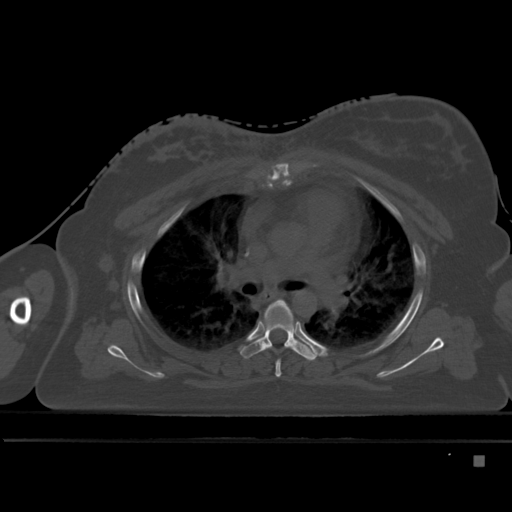
CT including the spine, one axial slice; position 324 of 495 along the scan axis; bone window (W 1800 / L 400 HU); 512 × 512 image matrix. Female patient, age 33 years. Case-level facts recorded for this patient, not image findings: primary cancer: breast; vertebrae with lytic lesions (as recorded): T1.
Outlined on this slice (semi-automatic segmentation, software-assisted and operator-edited):
- T4 vertebra: bounding box <275,322,296,378> (left, top, right, bottom; pixels)
- T5 vertebra: <240,301,316,361>